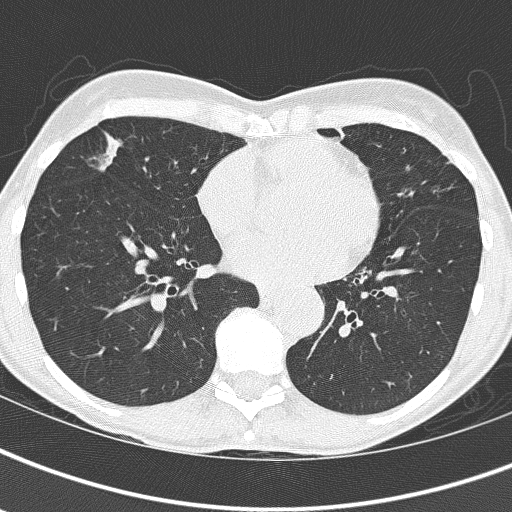
Low-dose screening chest CT, axial slice, first (baseline) screen, lung window (W 1500 / L -600 HU), 2 mm slice thickness, 512 × 512 image matrix, field of view 290 × 290 mm. Female participant, aged 67 years at enrolment.
Lesion marked by an expert reader, bounding box [x1, y1, x2, y2] px = [84, 123, 178, 205]. No non-calcified nodule or mass ≥4 mm was recorded by the screening reader at this exam. Participant outcome: lung cancer diagnosed 832 days after this screen (after the third annual screen) — bronchiolo-alveolar adenocarcinoma, NOS, right middle lobe, well differentiated (G1), stage IA (AJCC 6th edition), 25 mm at pathology.